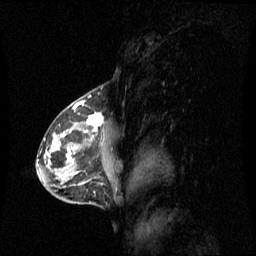
Breast MRI (dynamic contrast-enhanced), one sagittal slice. Slice 39 of 60 in the series (ordered by position). Dynamic contrast-enhanced series, image 2 of 3 at this slice position (ordered by acquisition). 1.5 T. TE 4.2 ms, TR 8.4 ms. 2 mm slice thickness. 256 × 256 image matrix. Female patient, age 42 years. From the clinical record (not read from this slice): setting: breast cancer imaged before/during neoadjuvant chemotherapy; receptor status: HR-positive, HER2-negative.
Annotated regions visible in this slice (semi-automatic segmentation, software-assisted and operator-edited):
- analysis volume of interest (the breast-tissue region the enhancement analysis was run in; not a lesion): bounding box (x1, y1, x2, y2) in pixels: (56, 113, 120, 185)
- tumour enhancement mask (voxels above the 70 % enhancement threshold inside the analysis volume of interest): (59, 113, 103, 162)